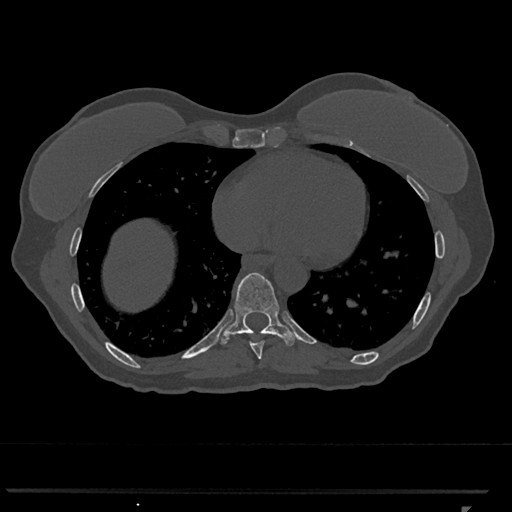
CT including the spine, one axial slice. 120 kVp. Bone window (W 1800 / L 400 HU). 0.5 mm slice thickness. 512 × 512 image matrix, field of view 380 × 380 mm. Patient: female, 62 years. Case-level facts recorded for this patient, not image findings: primary cancer: renal.
Structures marked on this image (semi-automatic segmentation, software-assisted and operator-edited):
- T8 vertebra: bounding box <250,341,265,359> (left, top, right, bottom; pixels)
- T9 vertebra: <221,272,300,346>